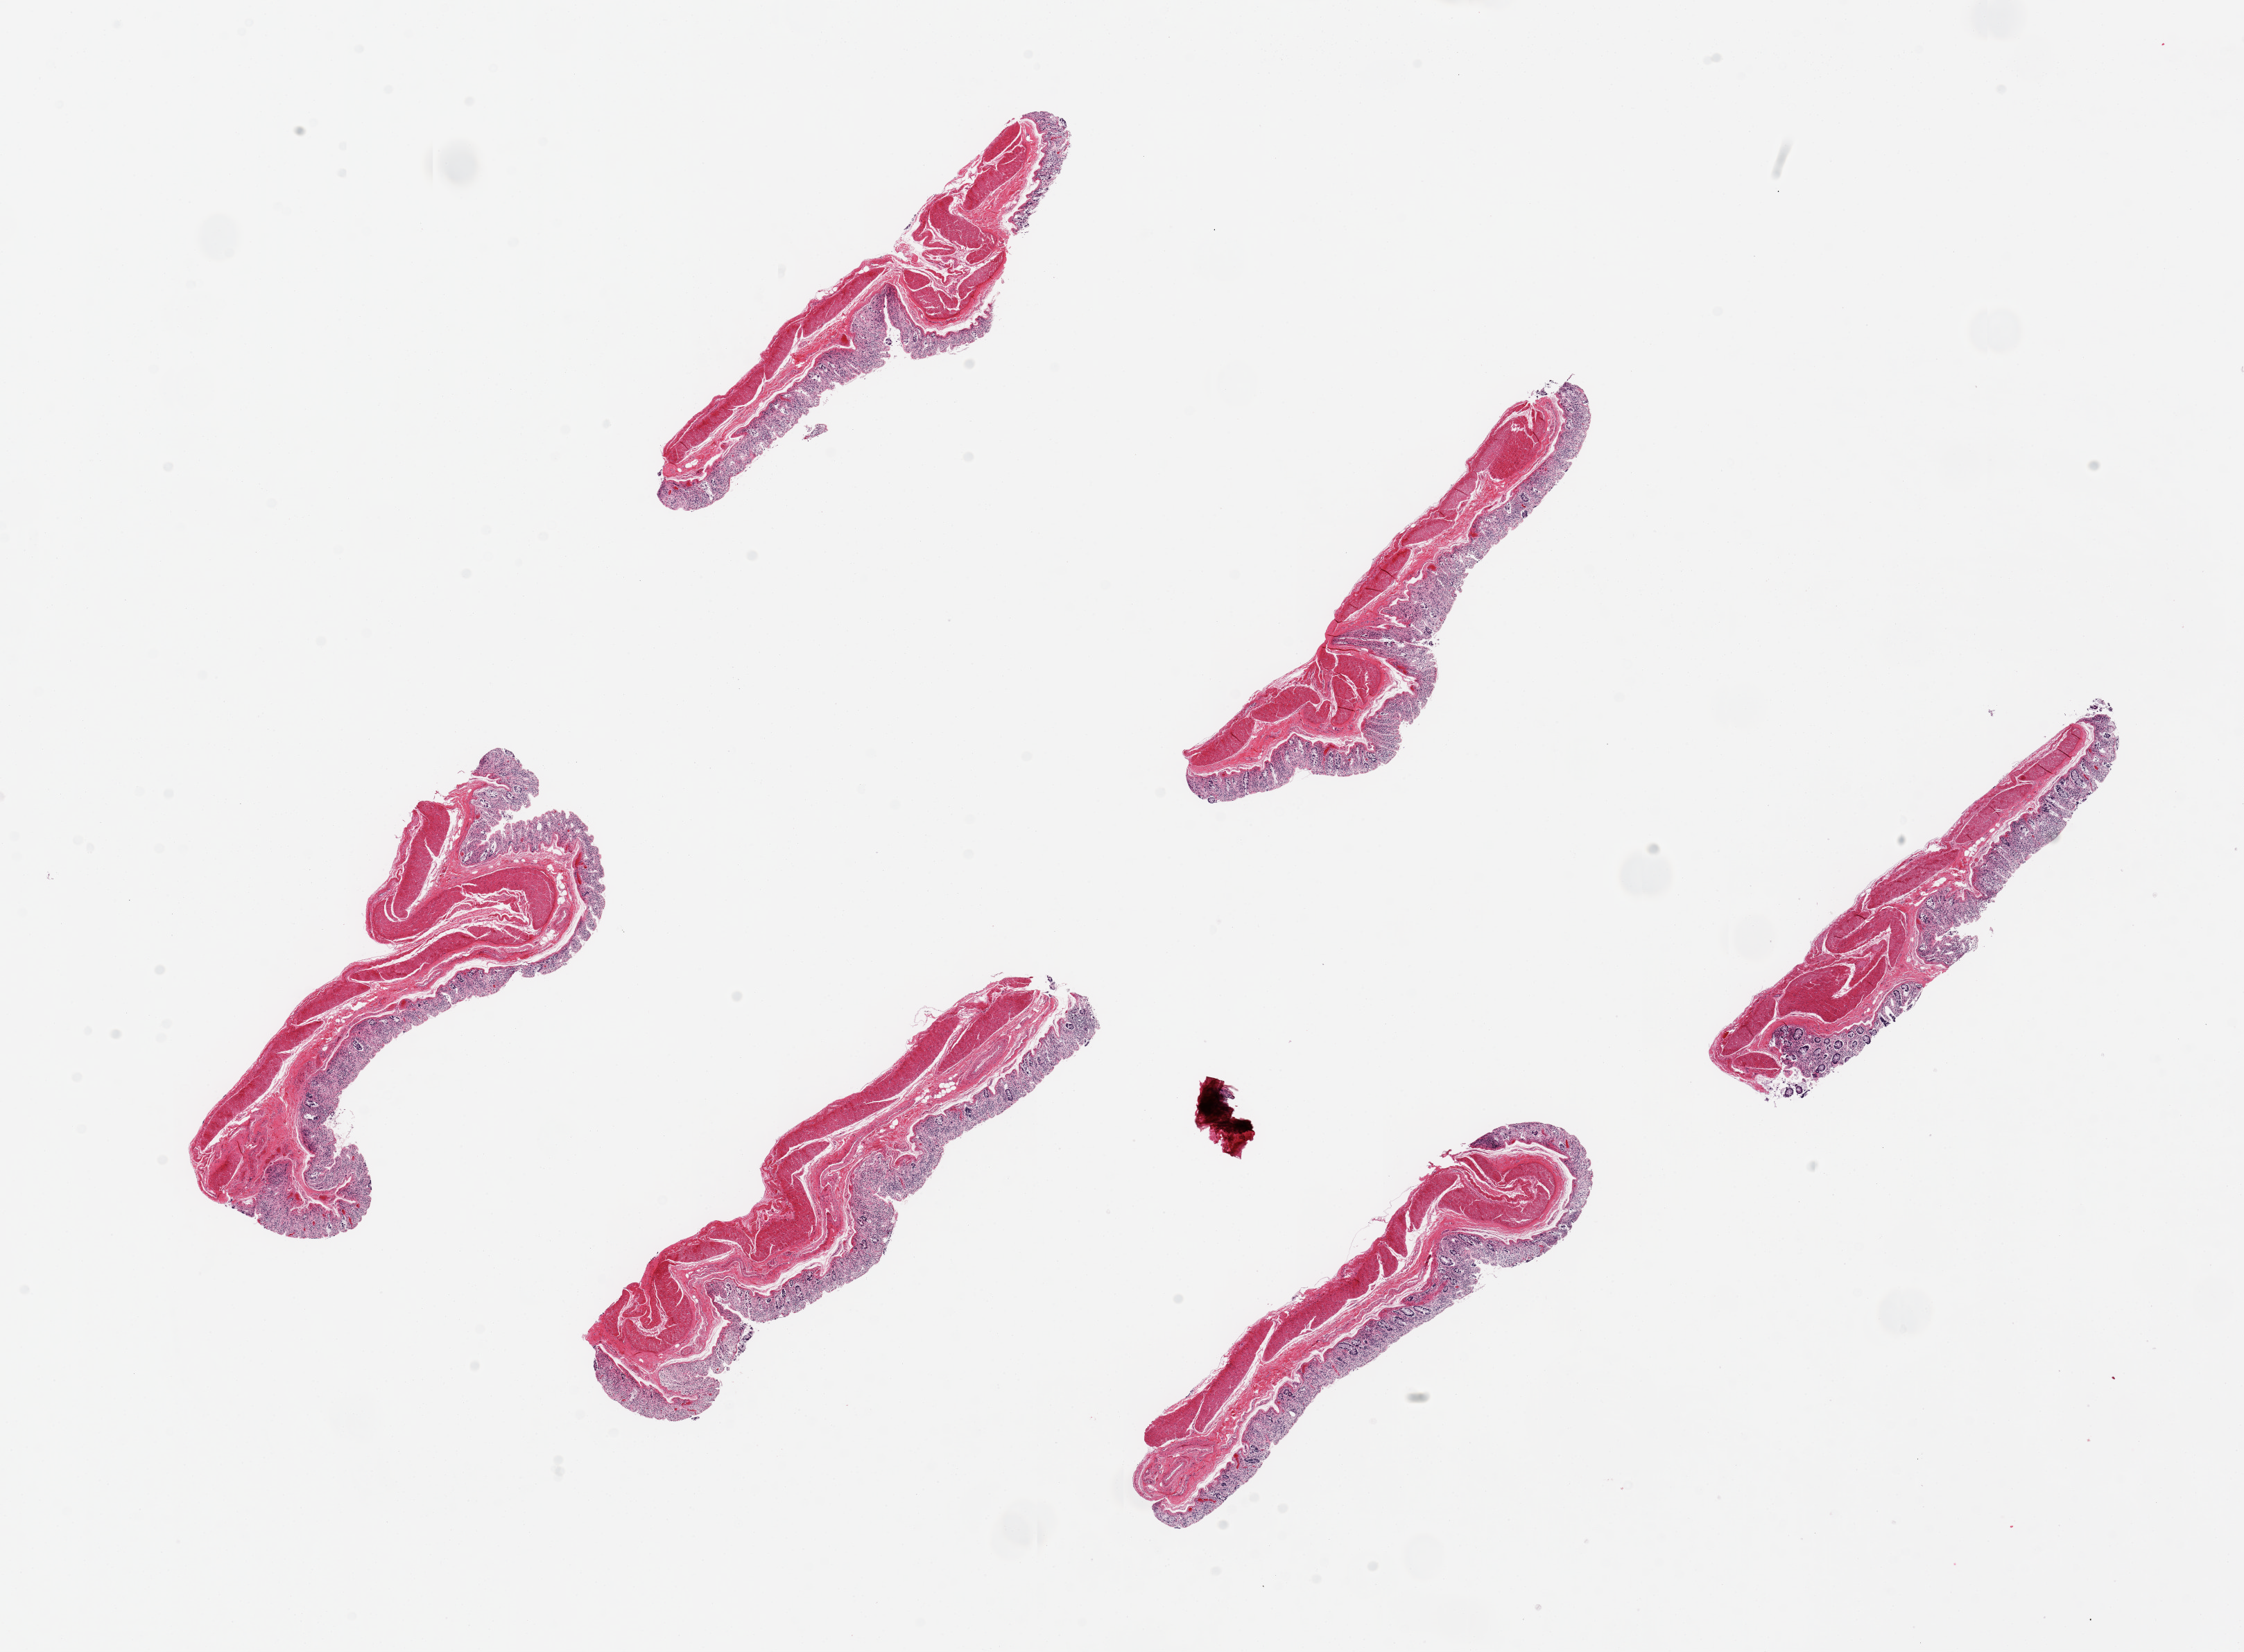
H&E whole-slide image, brightfield, a low-resolution overview of the entire scanned area, about 25.6 x 18.8 mm (from a 20x scan). PAXgene-fixed paraffin-embedded (PFPE) section. Target tissue: transverse colon. Donor tissue sample.
Reviewer comment on this tissue sample: 6 pieces. up to 7x2mm; mucosa=3; muscle= 2.